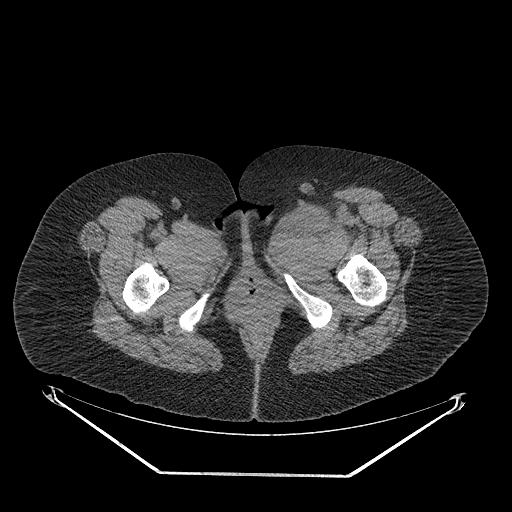
CT of an extremity soft-tissue mass (from a PET/CT study), one axial slice. Reconstruction kernel STANDARD. 140 kVp. Soft-tissue window (W 400 / L 40 HU). 512 × 512 image matrix, field of view 500 × 500 mm. Female patient. From the clinical record (not read from this slice): histological type: myxofibrosarcoma; grade: intermediate; site of the primary tumour: left thigh.
Structures marked on this image (expert contour drawn on MRI and transferred to this co-registered scan by the dataset authors):
- gross tumour volume including surrounding oedema: bounding box [x1, y1, x2, y2] px = [265, 203, 364, 254]
- gross tumour volume (mass): [288, 203, 332, 236]